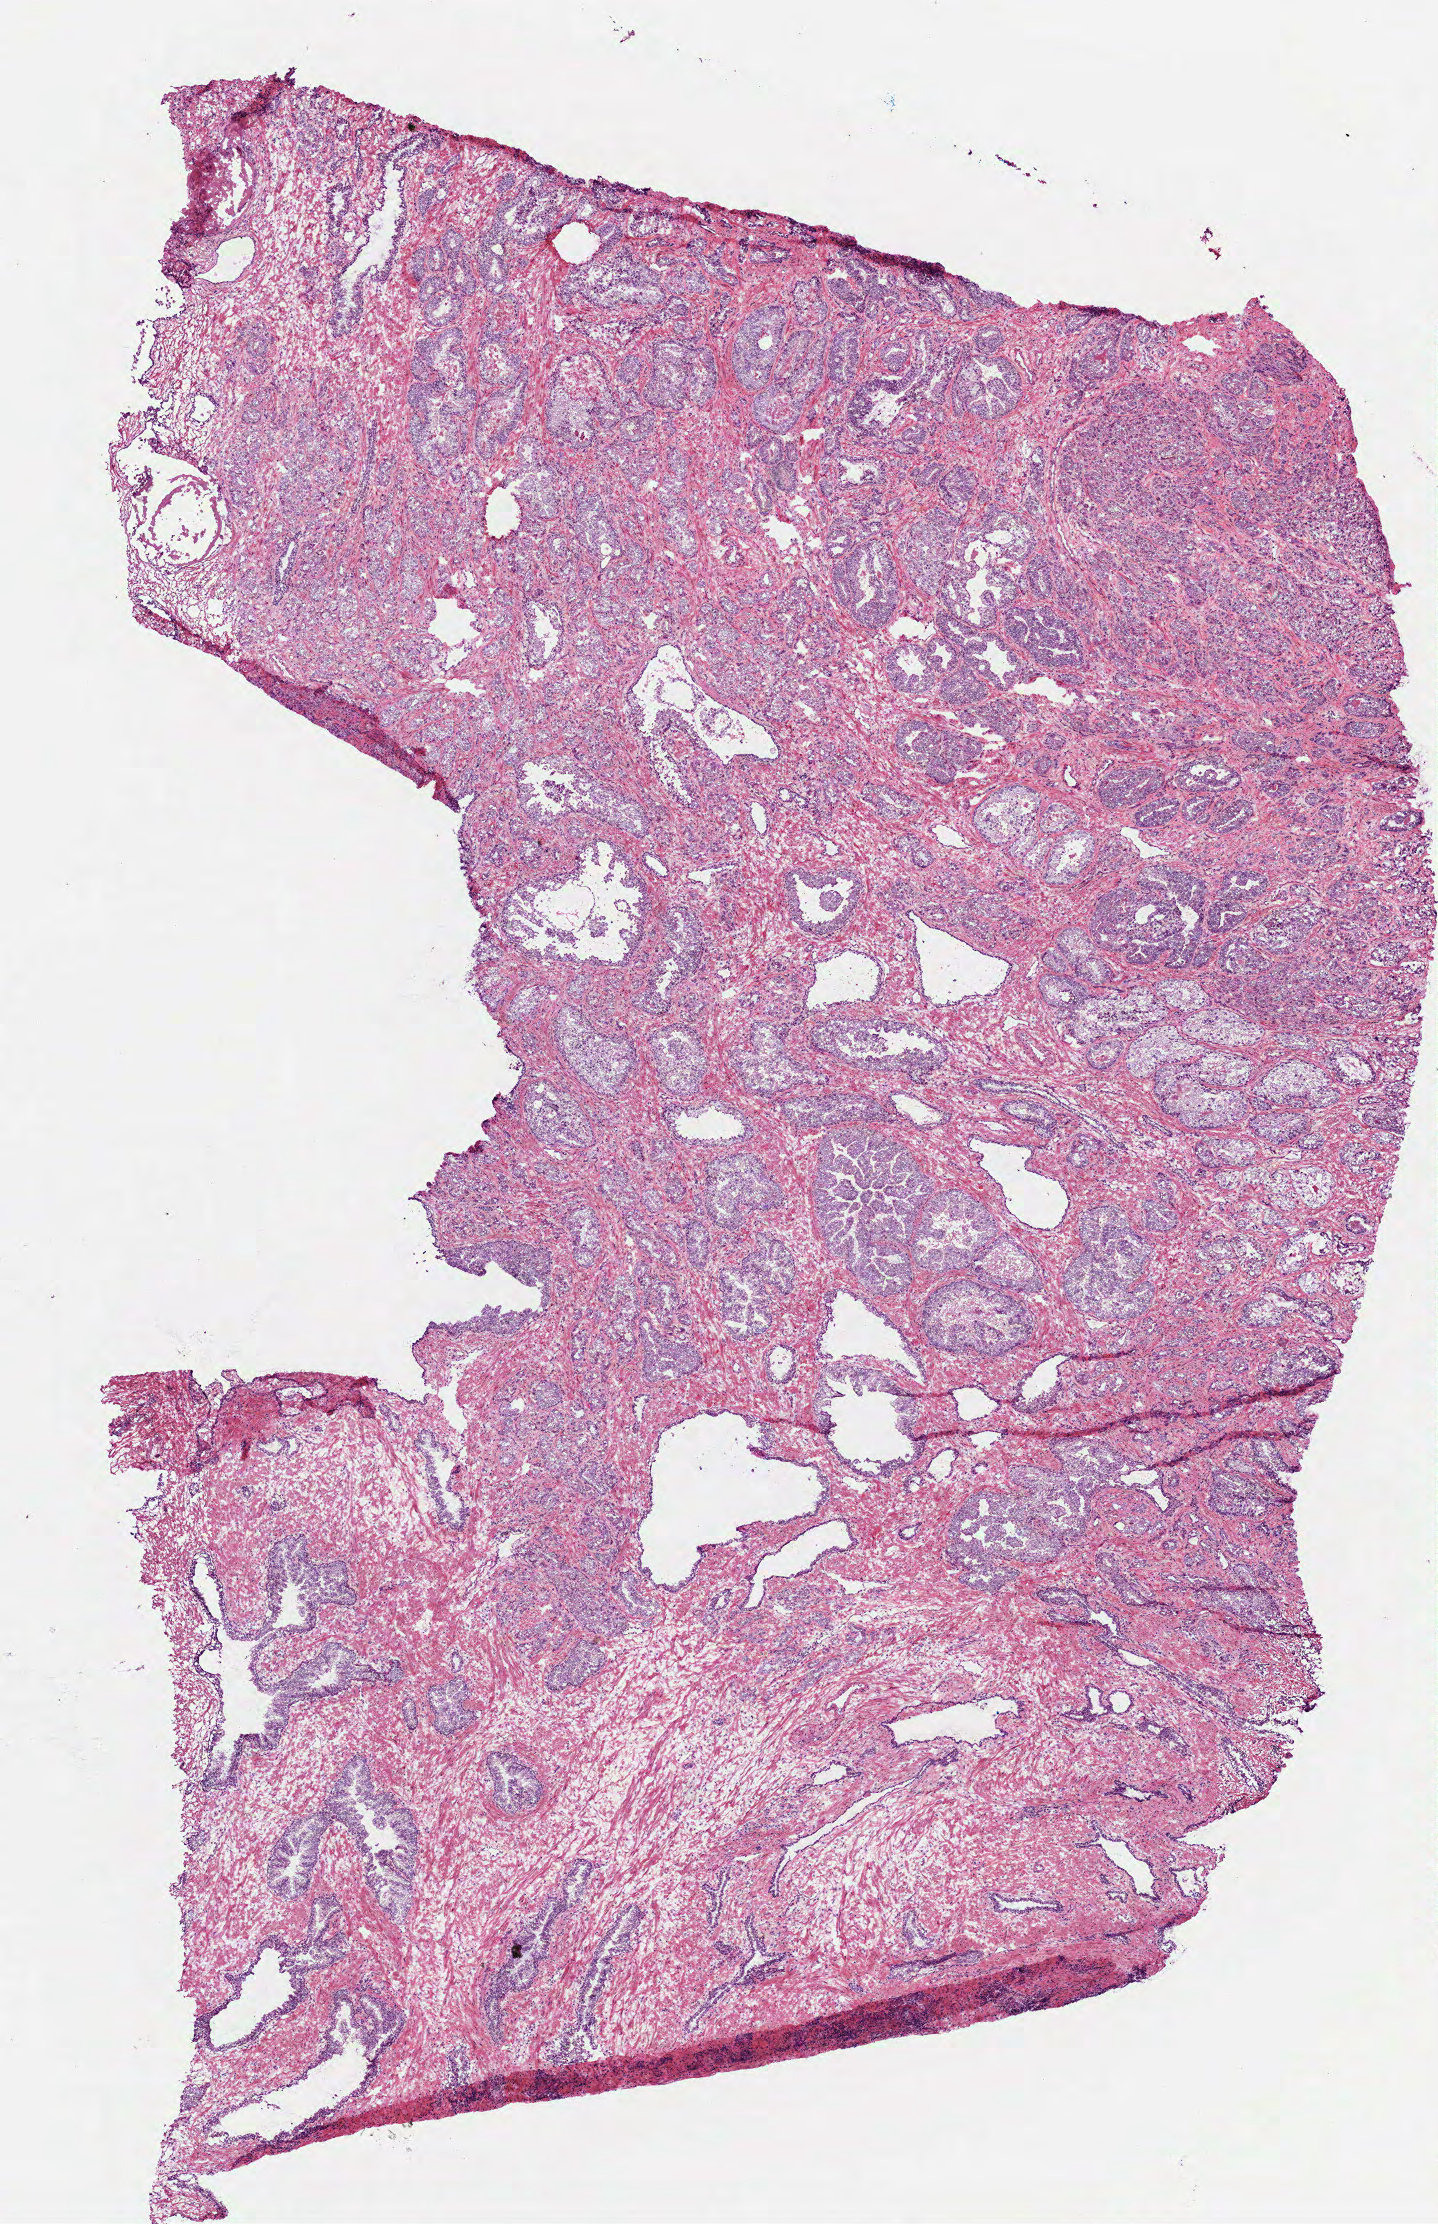
Digitized H&E-stained tissue section (whole slide), shown as a low-resolution overview of the whole scanned area (about 5.8 x 9.0 mm, from a 40x scan); frozen section from the bottom of the tissue portion; primary tumour sample from the prostate. Male, age 66 years at initial diagnosis. Gleason score: 9 (4+5).
Histologic diagnosis: Acinar cell carcinoma (prostate gland).